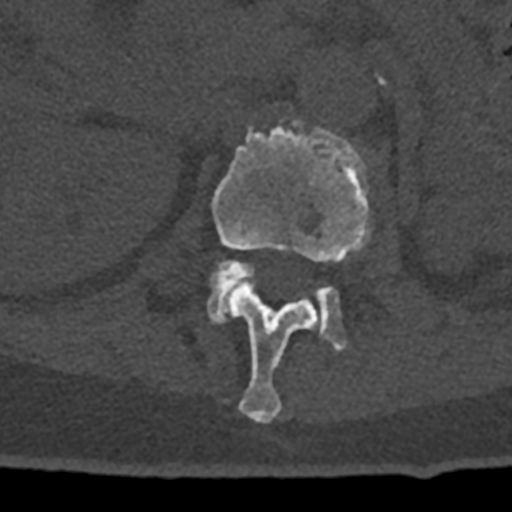
CT including the spine, one axial slice; position 417 of 797 along the scan axis; 120 kVp; bone window (W 1800 / L 400 HU); 0.5 mm slice thickness; 512 × 512 image matrix, field of view 160 × 160 mm. Patient: male, 74 years. Case-level facts recorded for this patient, not image findings: primary cancer: renal; vertebrae with lytic lesions (as recorded): T10, L1, L2, L3, L4, L5.
Structures marked on this image (semi-automatic segmentation, software-assisted and operator-edited):
- L1 vertebra: bounding box <212,120,372,424> (left, top, right, bottom; pixels)
- L2 vertebra: <207,260,347,350>